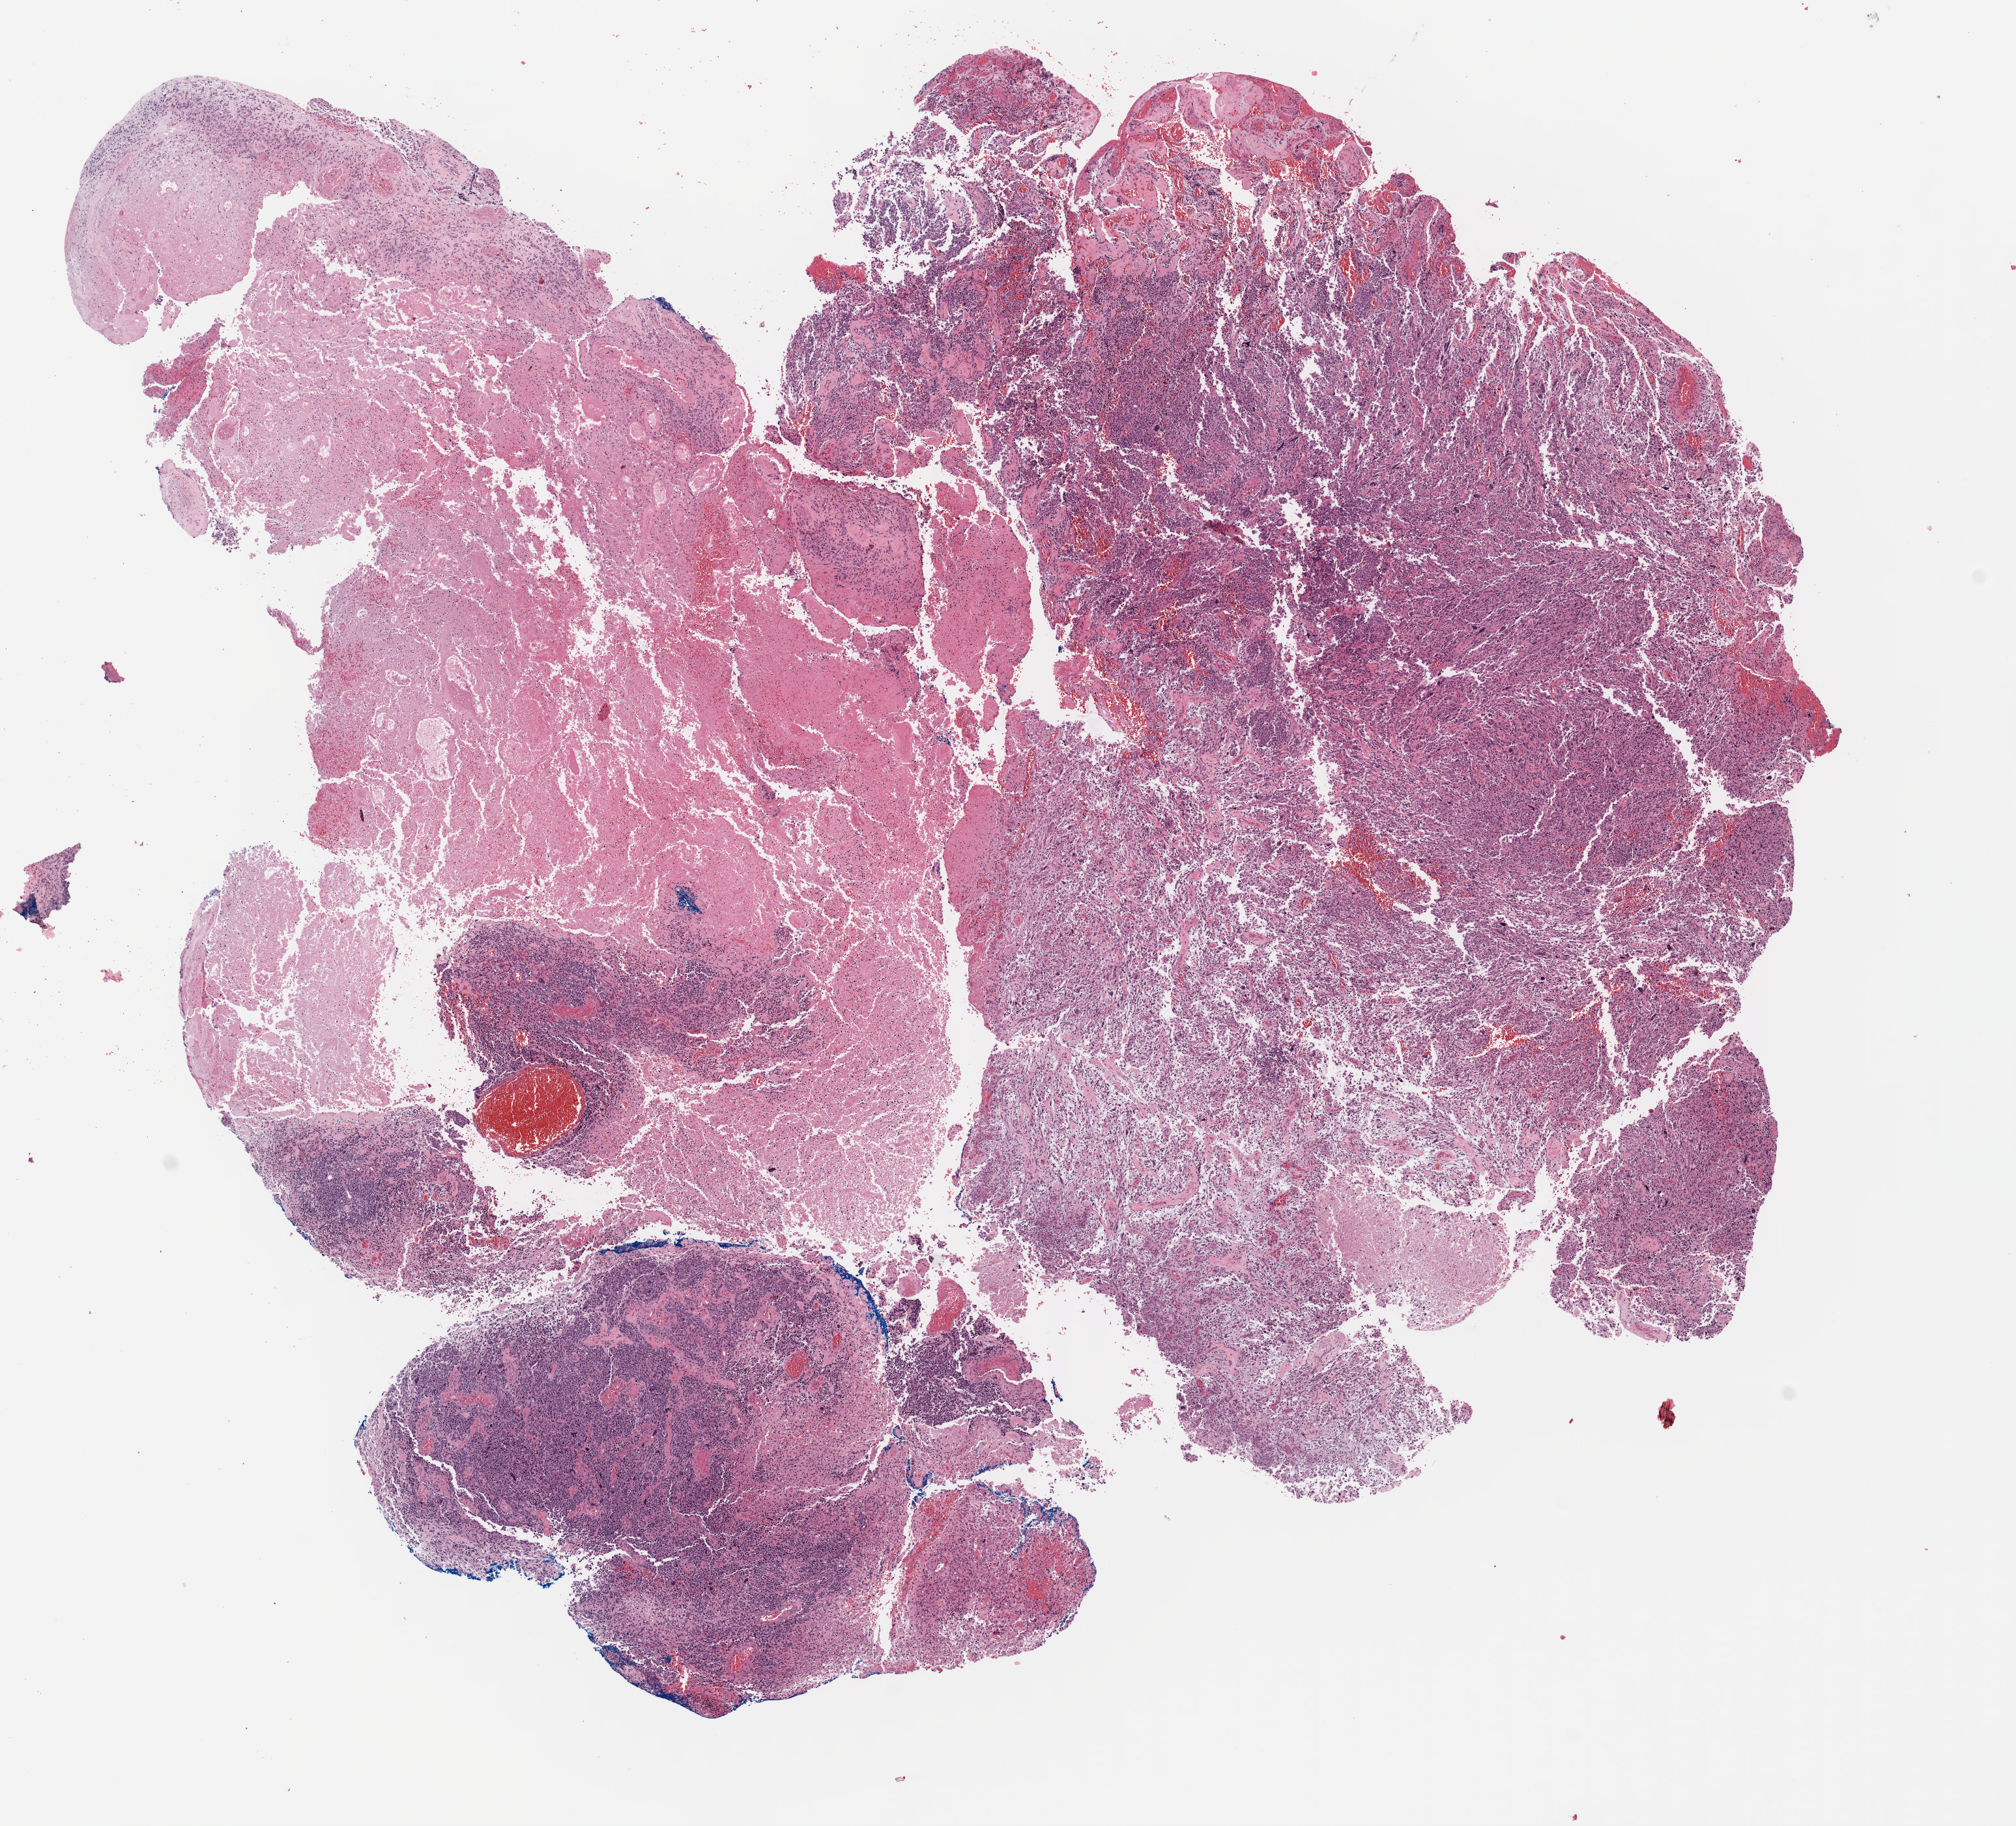
H&E whole-slide image, low-resolution overview of the scanned area, about 12.2 x 11.0 mm (from a 40x scan). Formalin-fixed paraffin-embedded (FFPE) diagnostic section. Primary tumour sample from the brain. Patient: male, age at initial diagnosis 39 years.
* pathologic diagnosis: Glioblastoma